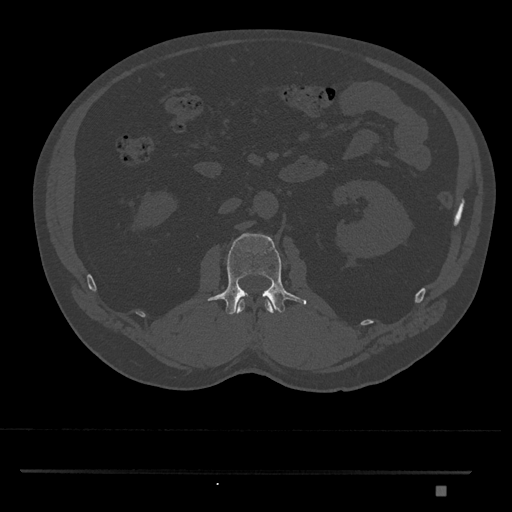
CT including the spine, one axial slice; reconstruction kernel Br40s/3; 120 kVp; bone window (W 1800 / L 400 HU); 0.5 mm slice thickness; 512 × 512 image matrix, field of view 429 × 429 mm. Male patient, age 65 years. Case-level facts recorded for this patient, not image findings: primary cancer: prostate.
Outlined on this slice (semi-automatic segmentation, software-assisted and operator-edited):
- L1 vertebra: bounding box (x1, y1, x2, y2) in pixels: (235, 298, 275, 315)
- L2 vertebra: (208, 233, 307, 315)